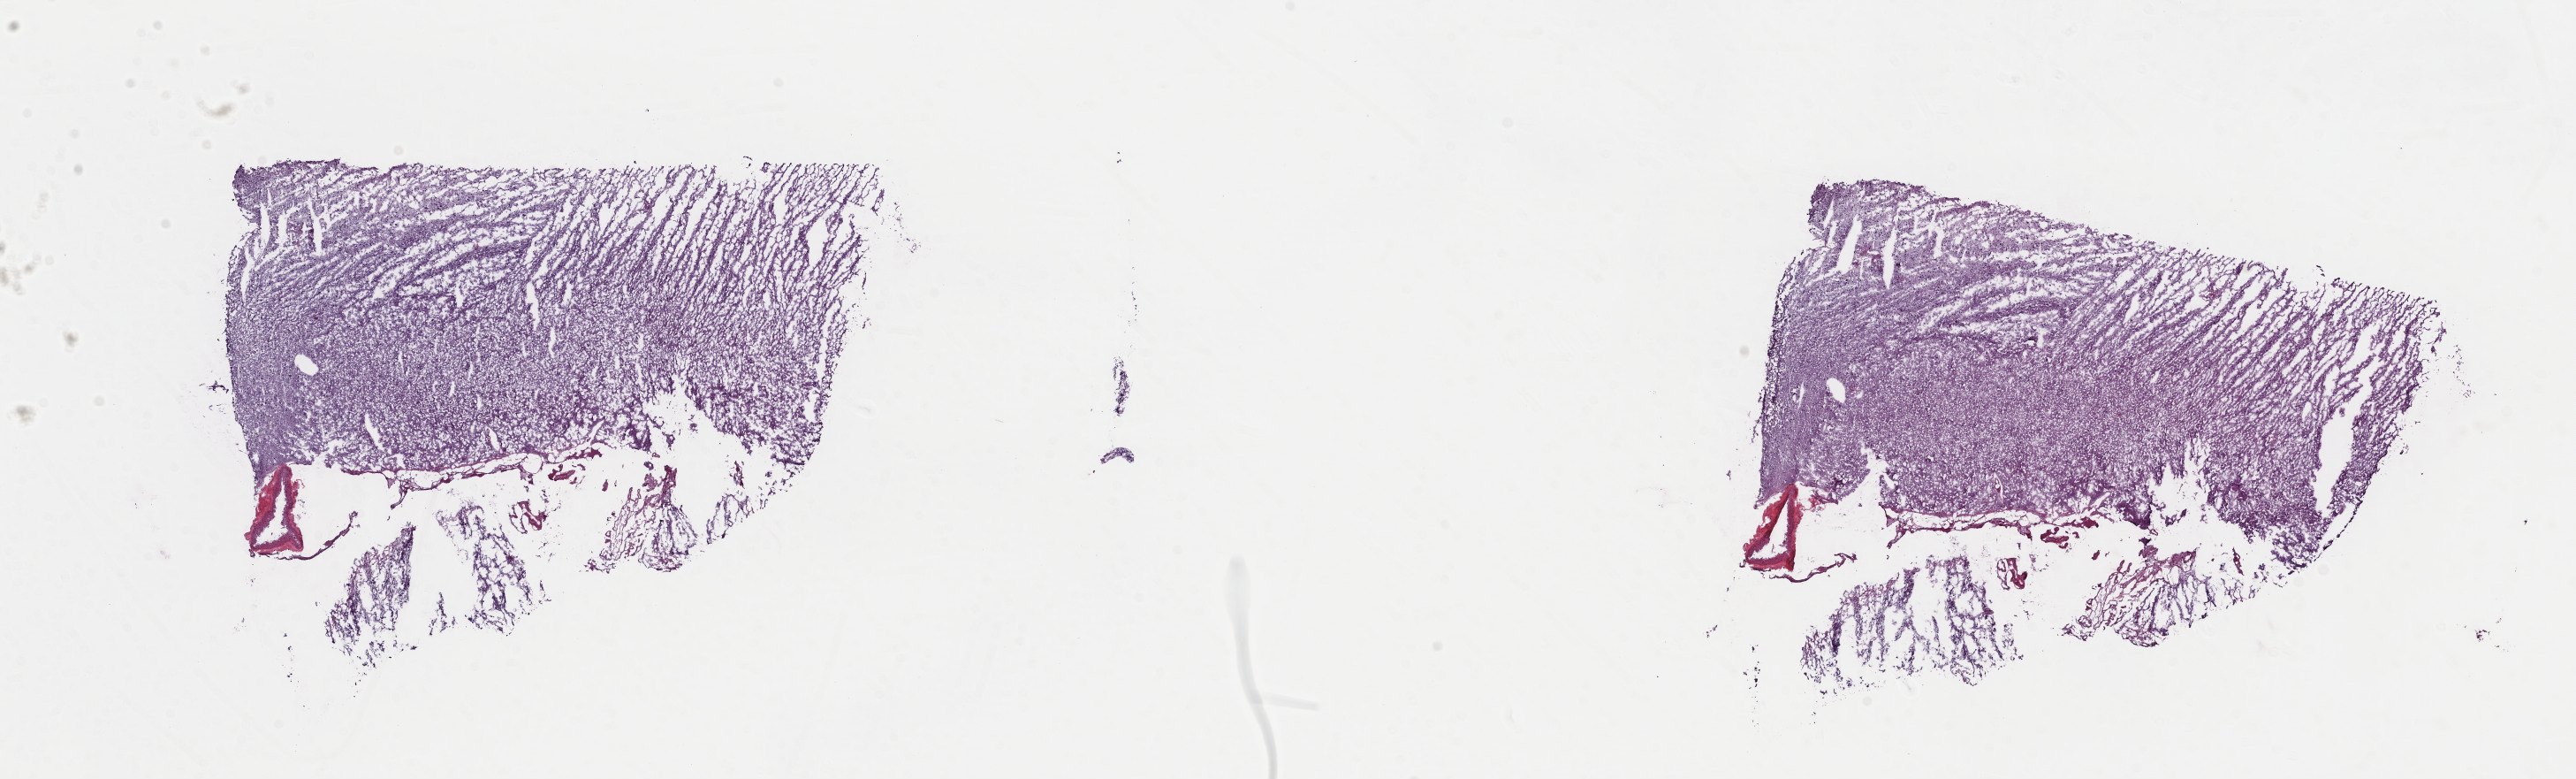
H&E whole-slide image — shown as a low-resolution overview of the whole scanned area (about 23.0 x 7.0 mm, from a 40x scan); frozen section from the top of the tissue portion; primary tumour sample from the brain. Patient: female, age at initial diagnosis 35 years. Histologic grade: G3 (poorly differentiated). Pathologist review of this section (percent, as recorded): tumour cells 30%, tumour nuclei 80%, normal cells 10%, stromal cells 60%, necrosis 0%. Inflammatory infiltration, as recorded: lymphocyte infiltration 0%, monocyte infiltration 0%, neutrophil infiltration 0%.
Diagnosis: Oligodendroglioma, anaplastic (cerebrum). Laterality: right.